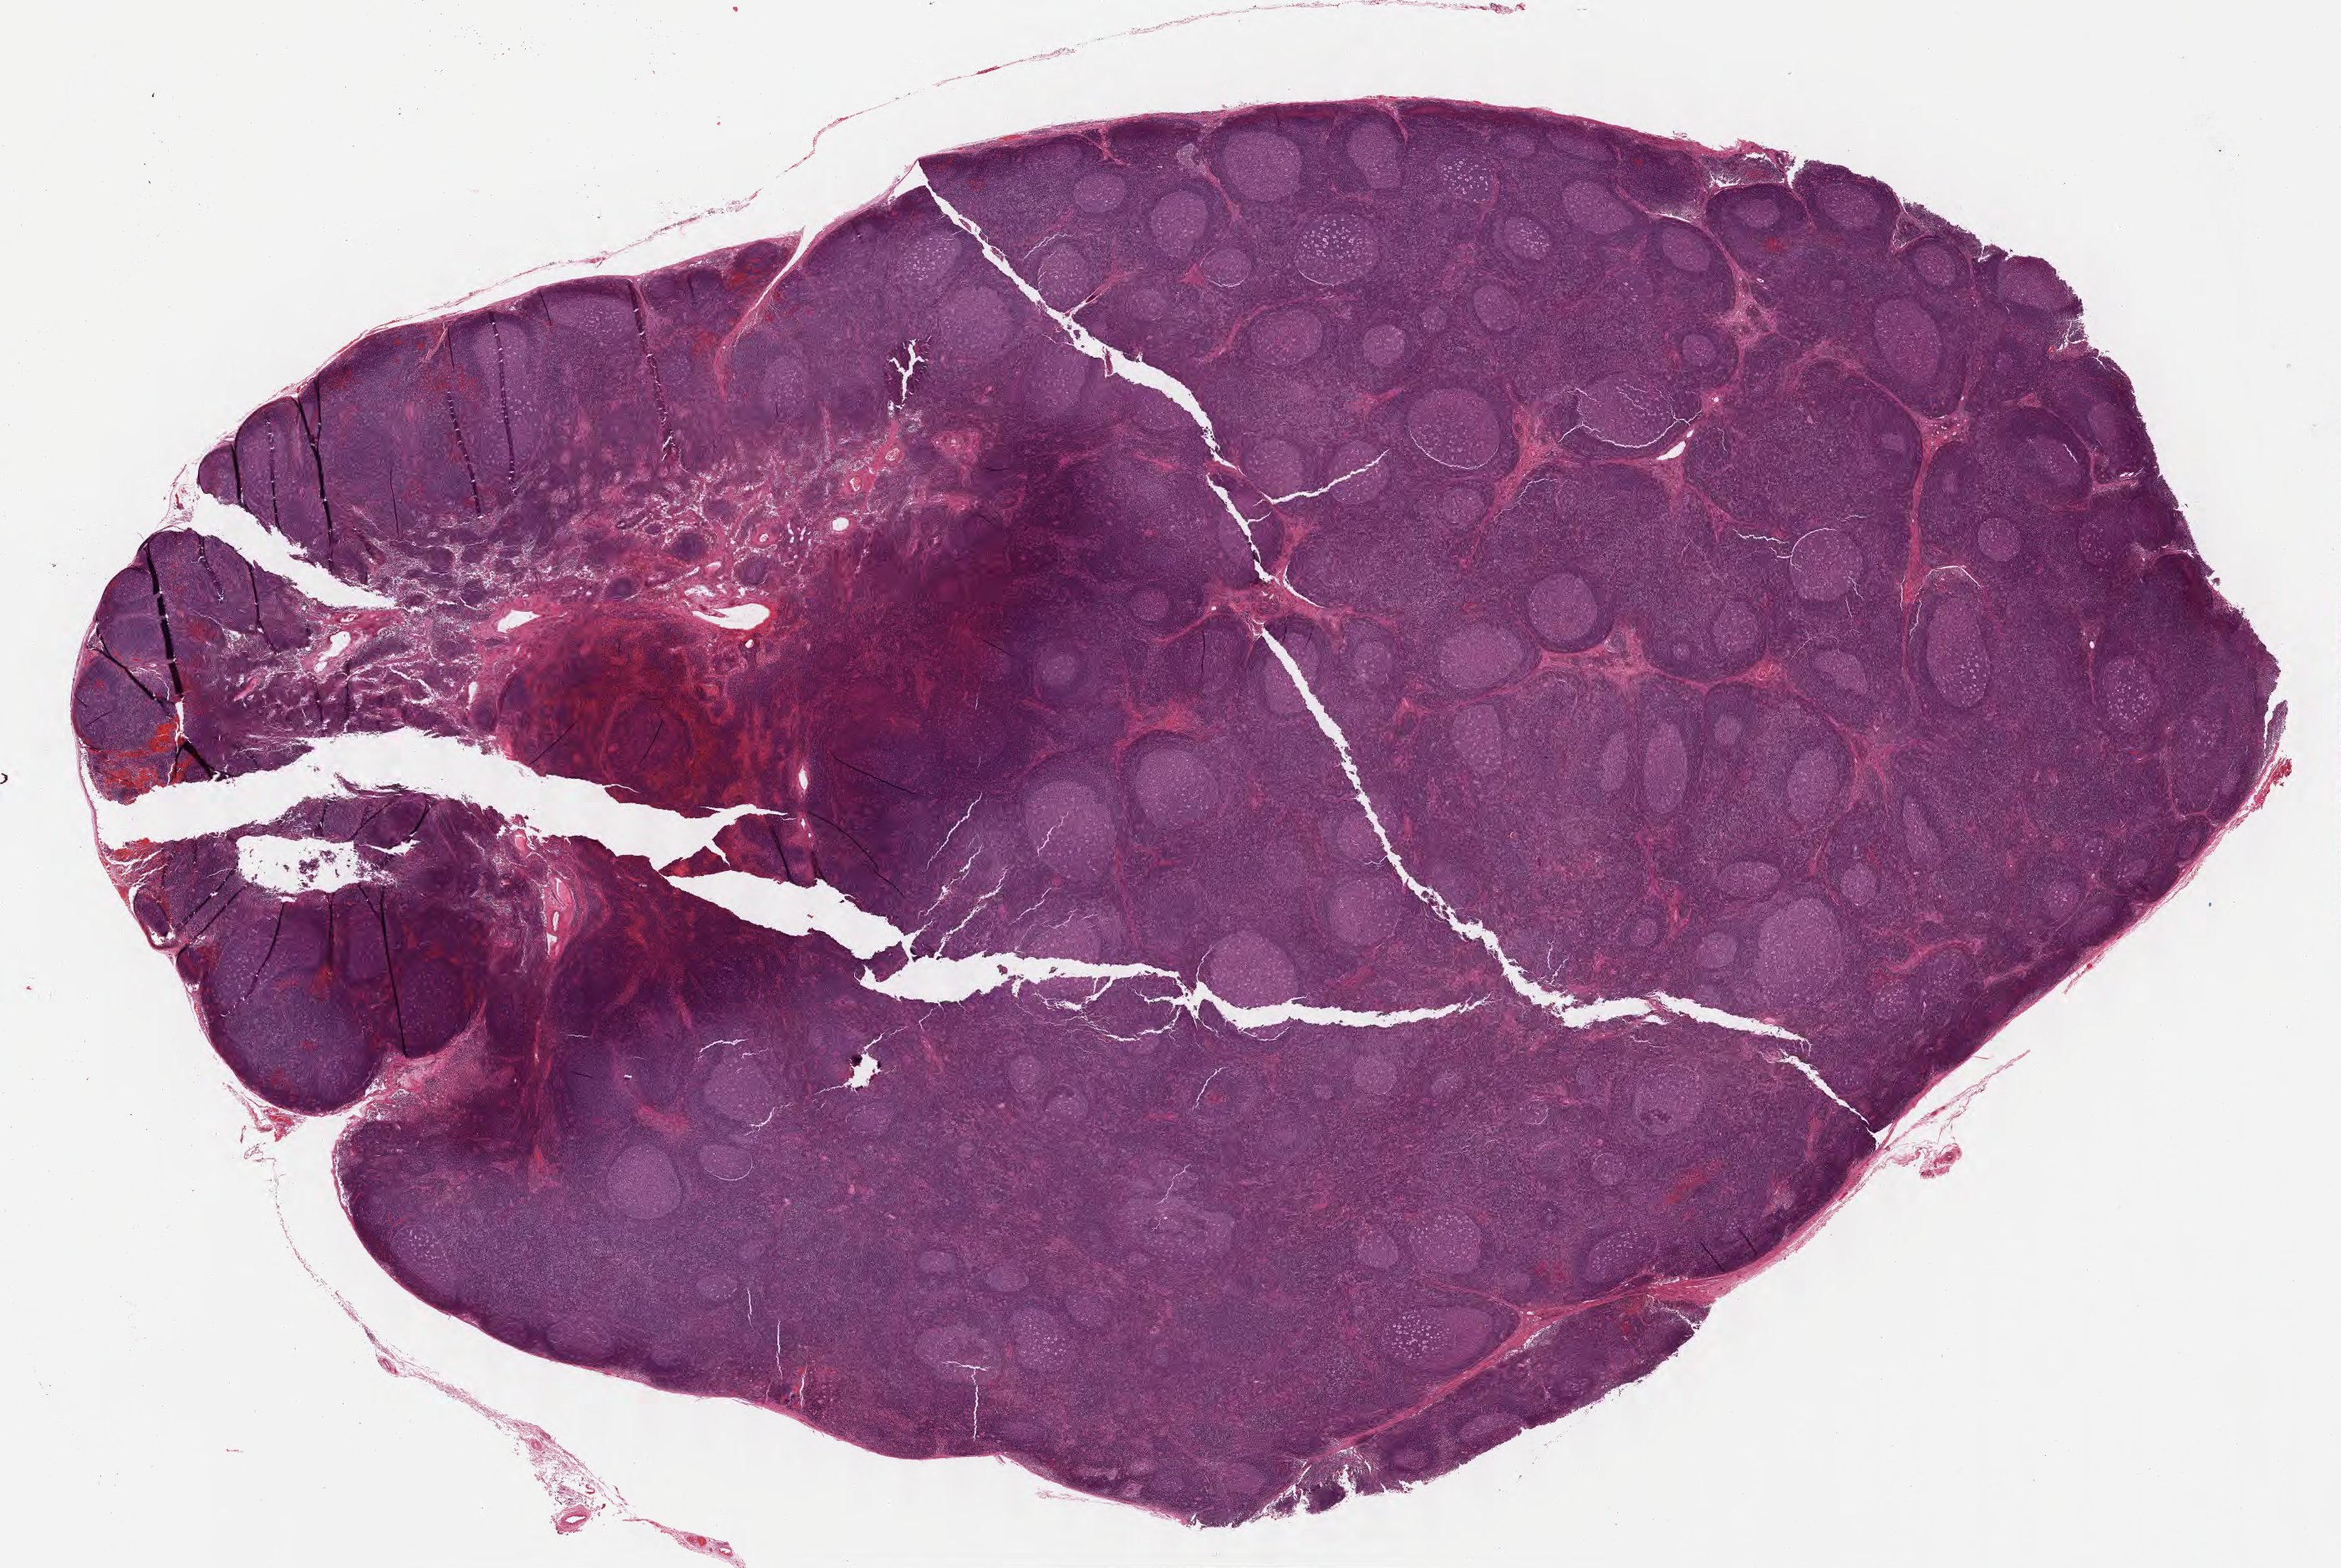
Whole-slide image, haematoxylin and eosin stain — low-resolution overview of the scanned area, about 22.6 x 15.2 mm, FFPE section, specimen: normal-tissue sample (non-tumor) from a patient with burkitt lymphoma, NOS. Male patient; age at initial diagnosis 4 years. Composition of this section per pathologist review: tumor cells 0%, tumor nuclei 0%, stromal cells 0%, necrosis 0%, normal cells 100%. Inflammatory infiltration, as recorded: lymphocyte infiltration 90%, monocyte infiltration 5%, neutrophil infiltration 0%.
This section: non-tumor tissue sample; the patient's diagnosis is given above.